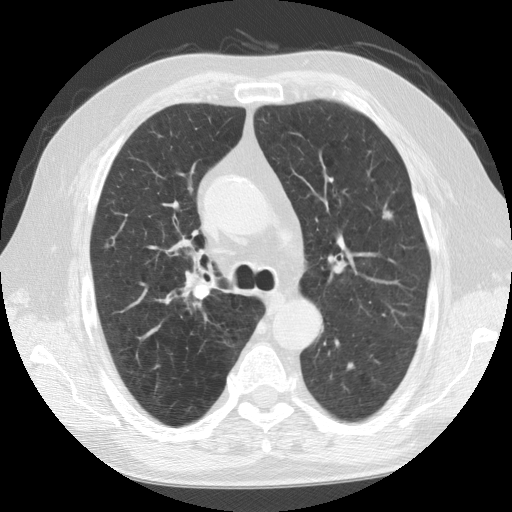
Low-dose screening chest CT, one axial slice. Position 68 of 109 along the scan axis. 120 kVp. Lung window (W 1500 / L -600 HU). 2.5 mm slice thickness. 512 × 512 image matrix.
Outlined on this slice (manually delineated by an expert):
- lesion 1 (tumor, upper lobe of left lung): bounding box <382,209,393,219> (left, top, right, bottom; pixels)